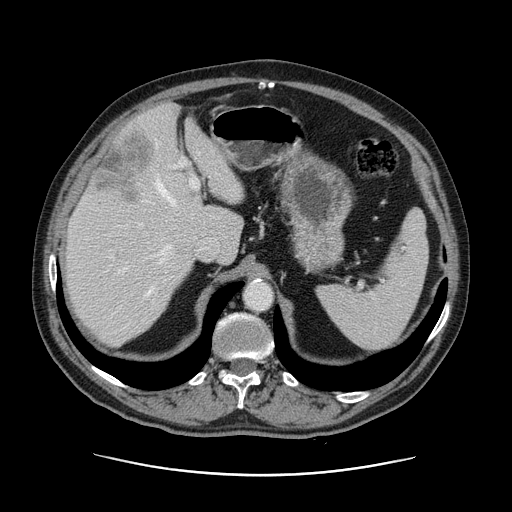
Contrast-enhanced abdominal CT, one axial slice; slice 88 of 141 in the series (ordered by position); intravenous contrast given; soft-tissue window (W 400 / L 40 HU); 2.5 mm slice thickness; 512 × 512 image matrix, field of view 395 × 395 mm. Male patient, age 72 years. Case-level facts recorded for this patient, not image findings: diagnosis: colorectal cancer liver metastases, imaged before liver resection; multiple liver metastases: yes; largest metastasis: 5.4 cm.
Outlined on this slice (expert manual segmentation):
- hepatic veins: bounding box (x1, y1, x2, y2) in pixels: (145, 177, 176, 297)
- liver: (65, 104, 244, 345)
- planned liver remnant (the part of the liver to remain after resection): (65, 105, 244, 345)
- portal vein (with intrahepatic branches): (119, 157, 199, 293)
- liver metastasis: (93, 126, 153, 206)